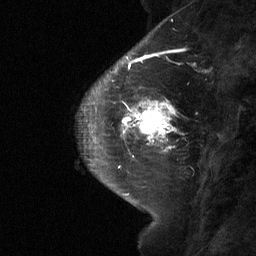
Breast MRI (dynamic contrast-enhanced), one sagittal slice. Position 19 of 64 along the scan axis. Dynamic contrast-enhanced study with each time point stored as its own series, time point 2 of 3 at this slice position (early post-contrast, ordered by acquisition time). 1.5 T. TE 4.8 ms, TR 27 ms. 2 mm slice thickness. 256 × 256 image matrix, field of view 180 × 180 mm. Patient: female, 42 years. From the clinical record (not read from this slice): setting: breast cancer imaged before/during neoadjuvant chemotherapy; receptor status: triple-negative.
Annotated regions visible in this slice (semi-automatically segmented with operator editing):
- analysis volume of interest (the breast-tissue region the enhancement analysis was run in; not a lesion): bounding box <115,85,177,160> (left, top, right, bottom; pixels)
- tumour enhancement mask (voxels above the 90 % enhancement threshold inside the analysis volume of interest): <122,98,171,157>